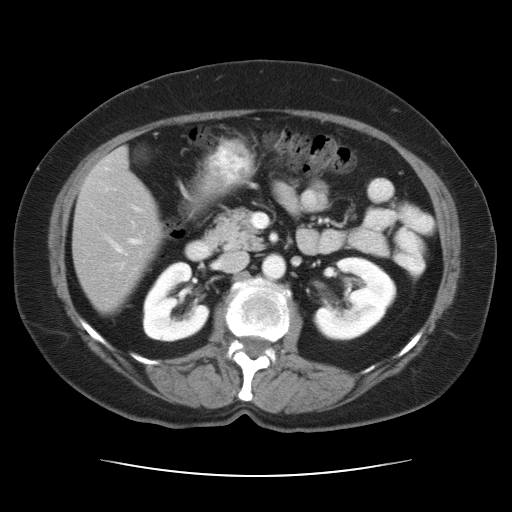
Contrast-enhanced abdominal CT, one axial slice; slice 13 of 34 in the series (ordered by position); reconstruction kernel STANDARD; 120 kVp; intravenous contrast given; soft-tissue window (W 400 / L 40 HU); 7.5 mm slice thickness; 512 × 512 image matrix, field of view 360 × 360 mm. Female patient, age 65 years. From the clinical record (not read from this slice): diagnosis: colorectal cancer liver metastases, imaged before liver resection; multiple liver metastases: yes; largest metastasis: 2.2 cm; disease in both lobes: no.
Annotated regions visible in this slice (manually delineated by an expert):
- hepatic veins: bounding box (x1, y1, x2, y2) in pixels: (111, 241, 122, 252)
- liver: (73, 151, 158, 309)
- planned liver remnant (the part of the liver to remain after resection): (73, 151, 158, 310)
- portal vein (with intrahepatic branches): (130, 239, 139, 244)